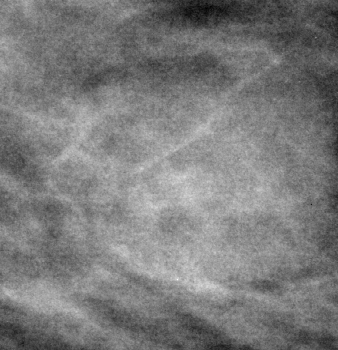
Region of interest cut from a scanned film mammogram (one marked finding); right breast; CC view.
Marked abnormality: mass, shape round, margins circumscribed; BI-RADS assessment category 4; pathology (as recorded): benign.